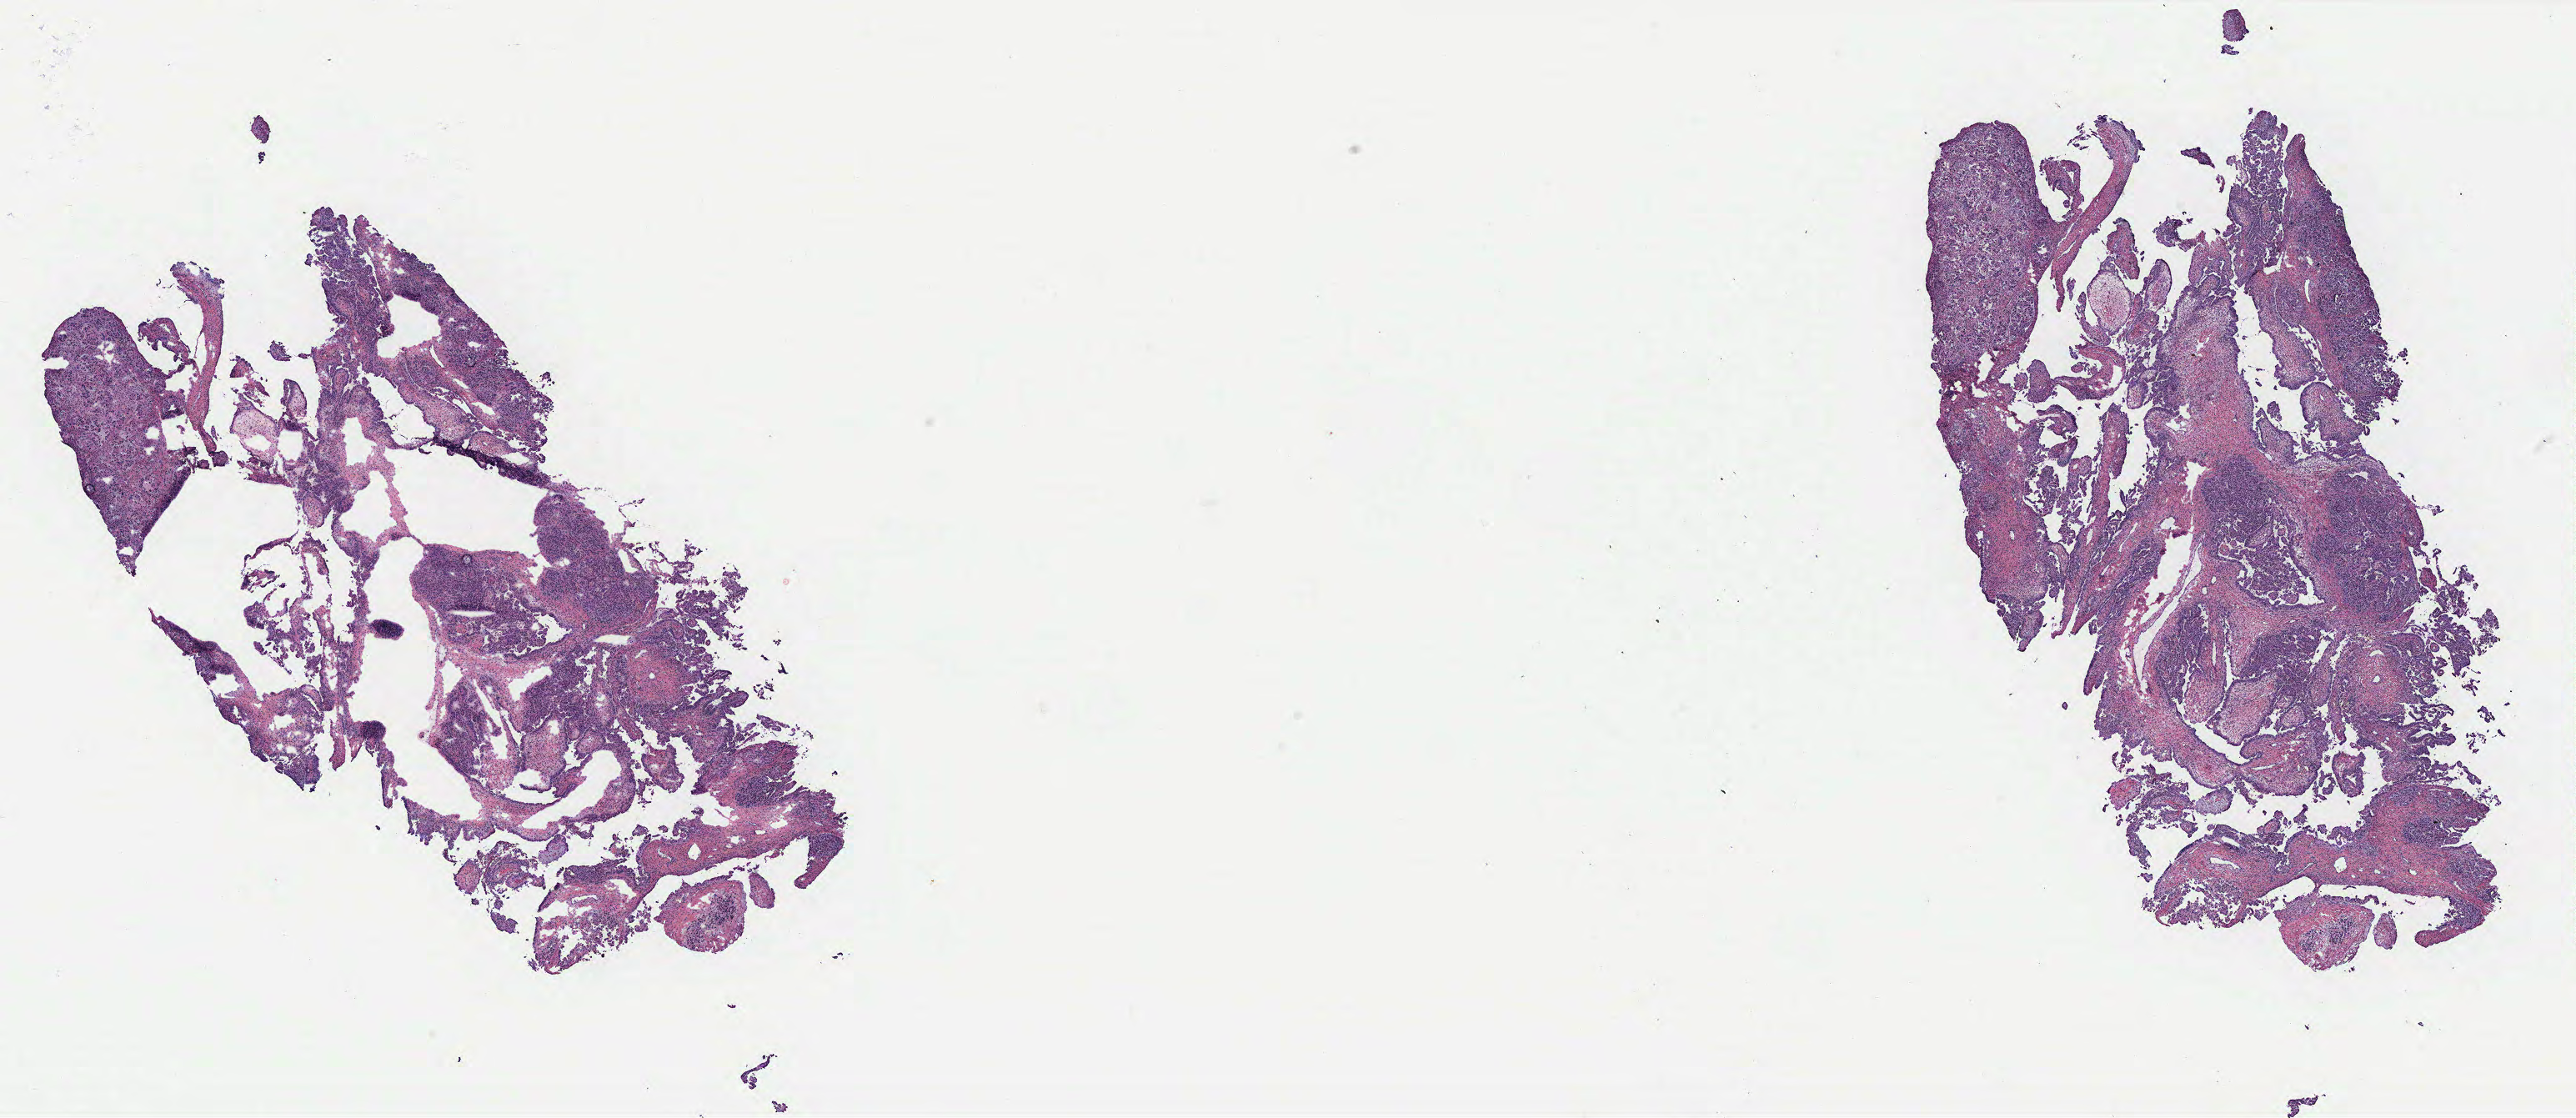
H&E-stained whole-slide image — low-resolution overview of the scanned area, about 24.7 x 10.7 mm; ovary, tumour tissue. Female, 58 y/o.
Primary tumour site (as recorded): ovary. Diagnosis: Serous adenocarcinoma, NOS.